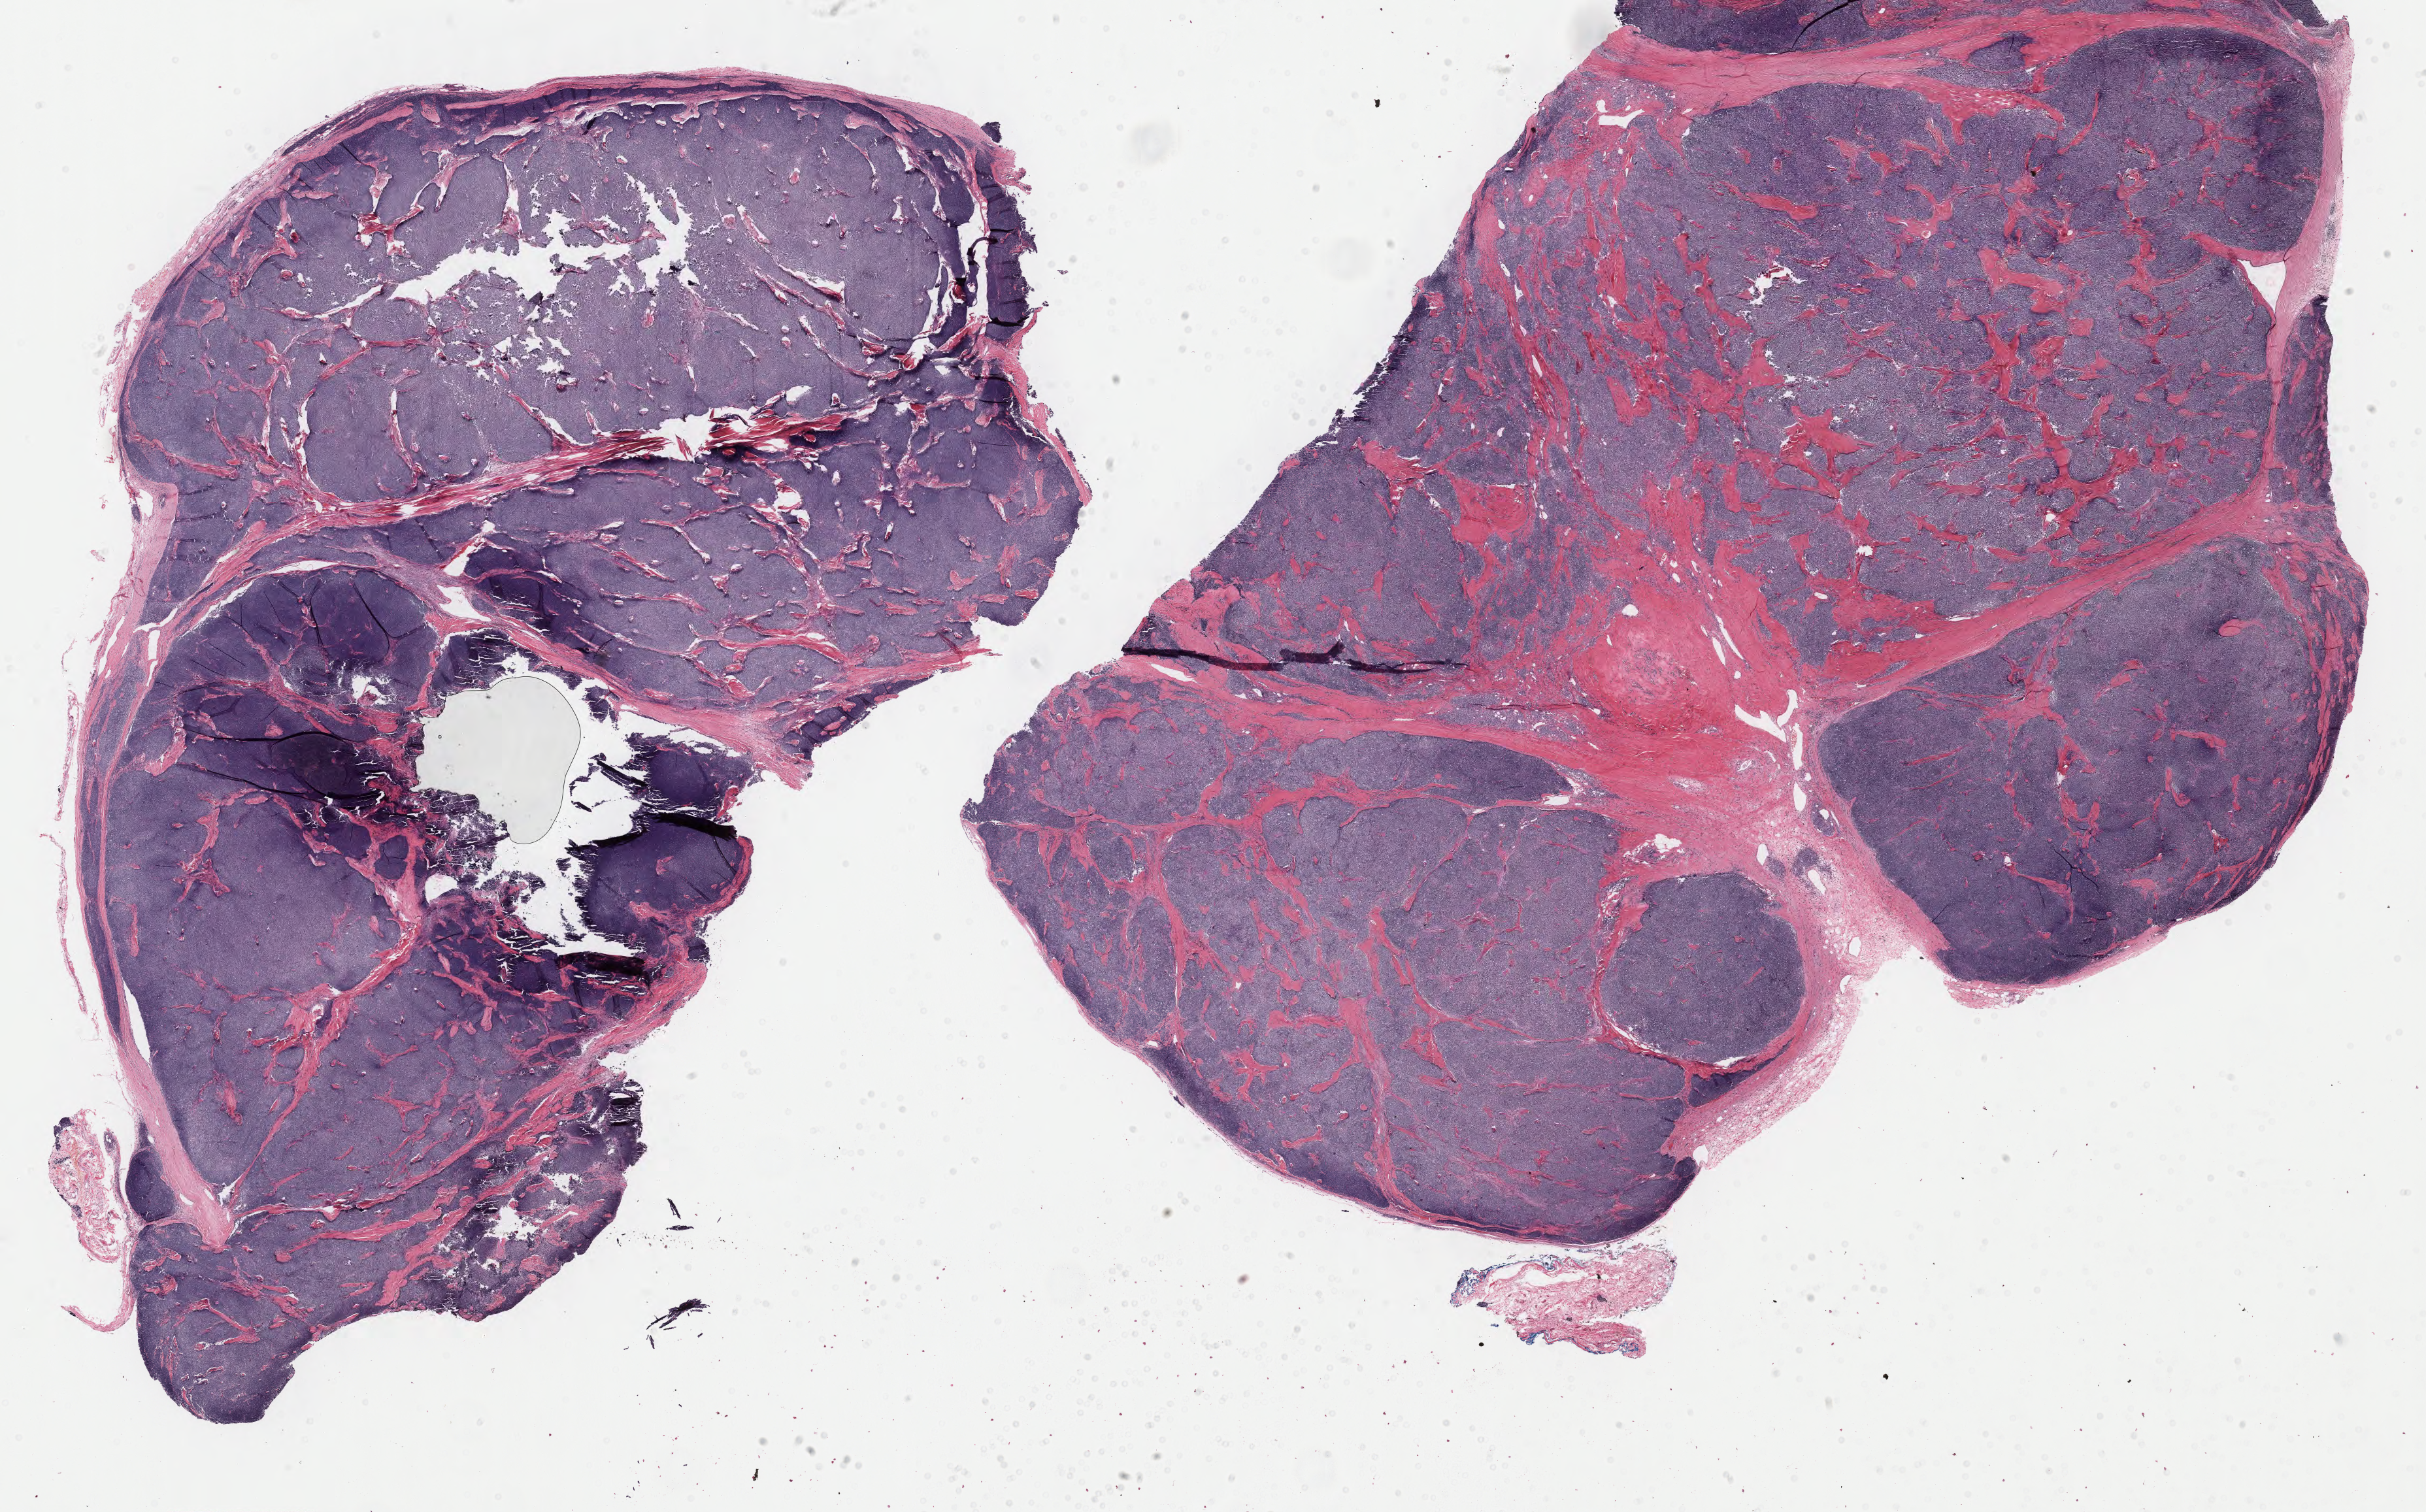
Whole-slide histology image, H&E-stained — shown as a low-resolution overview of the whole scanned area (about 29.4 x 18.3 mm), formalin-fixed paraffin-embedded (FFPE) diagnostic section, thymus, primary tumour sample. Female patient; age at initial diagnosis 50 years.
Histologic diagnosis: Thymoma, type AB, malignant.